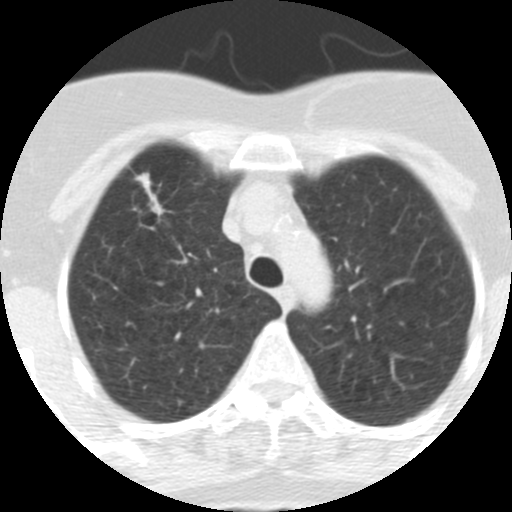
Chest CT (low-dose screening protocol), one axial image; first (baseline) screen; lung window (W 1500 / L -600 HU); standard (soft-tissue) reconstruction kernel (STANDARD); 120 kVp; slice 66 of 313 in the series; 512 × 512 image matrix. Female, age 62 years at enrolment. Current smoker at enrolment.
- Expert reader's lesion annotation, bounding box <116,167,187,236> (left, top, right, bottom; pixels).
- The exam's reader record, not a measurement of the box and not confirmed to be the same lesion: non-calcified nodule or mass ≥4 mm, right upper lobe, 9 × 7 mm, spiculated (stellate) margins, soft tissue attenuation.
- Official screen result: positive, change unspecified: nodule(s) >= 4 mm or enlarging nodule(s), mass(es), or other non-specific abnormalities suspicious for lung cancer.
- Participant outcome: lung cancer diagnosed 126 days after this screen — adenocarcinoma, NOS, right upper lobe, moderately differentiated (G2), stage IA (AJCC 6th edition), 18 mm at pathology.